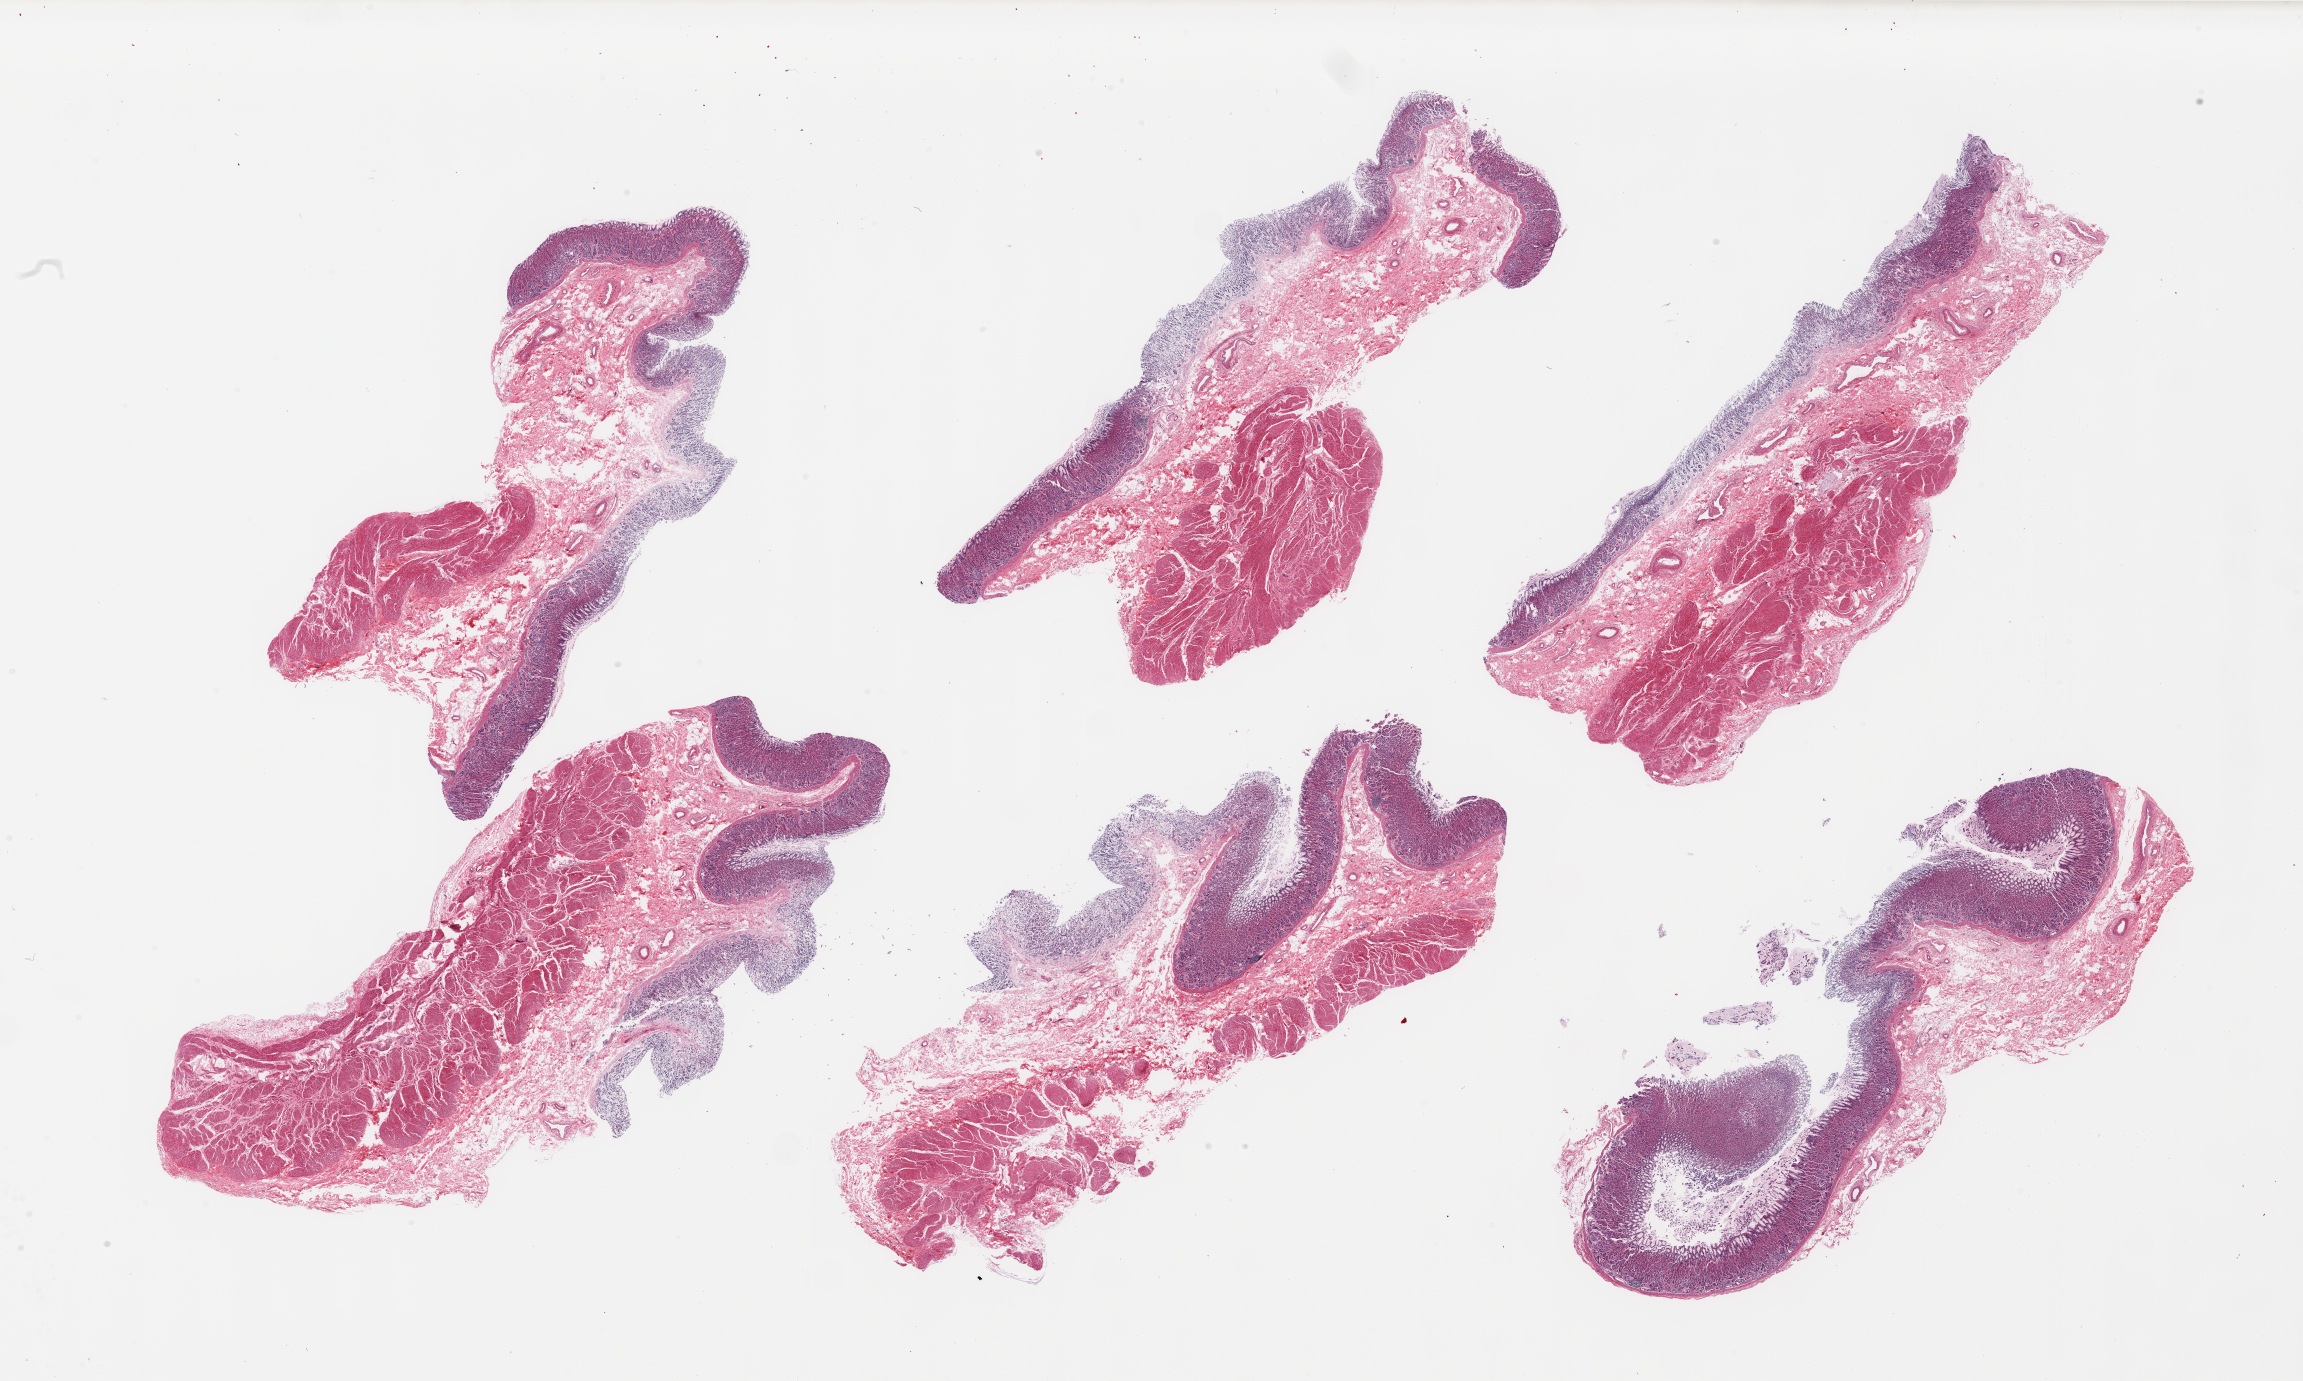
Whole-slide image, hematoxylin and eosin (H&E) stain, brightfield — whole scanned area (about 36.4 x 21.8 mm, slide scanned at 20x) shown as a low-resolution overview. PAXgene-fixed, paraffin-embedded tissue. Target tissue: stomach. Tissue donor sample. Donor sex: female.
Reviewer comment on this tissue sample: 6 pieces; mucosal autolysis varies from slight to severe; muscularis missing on 1 piece.